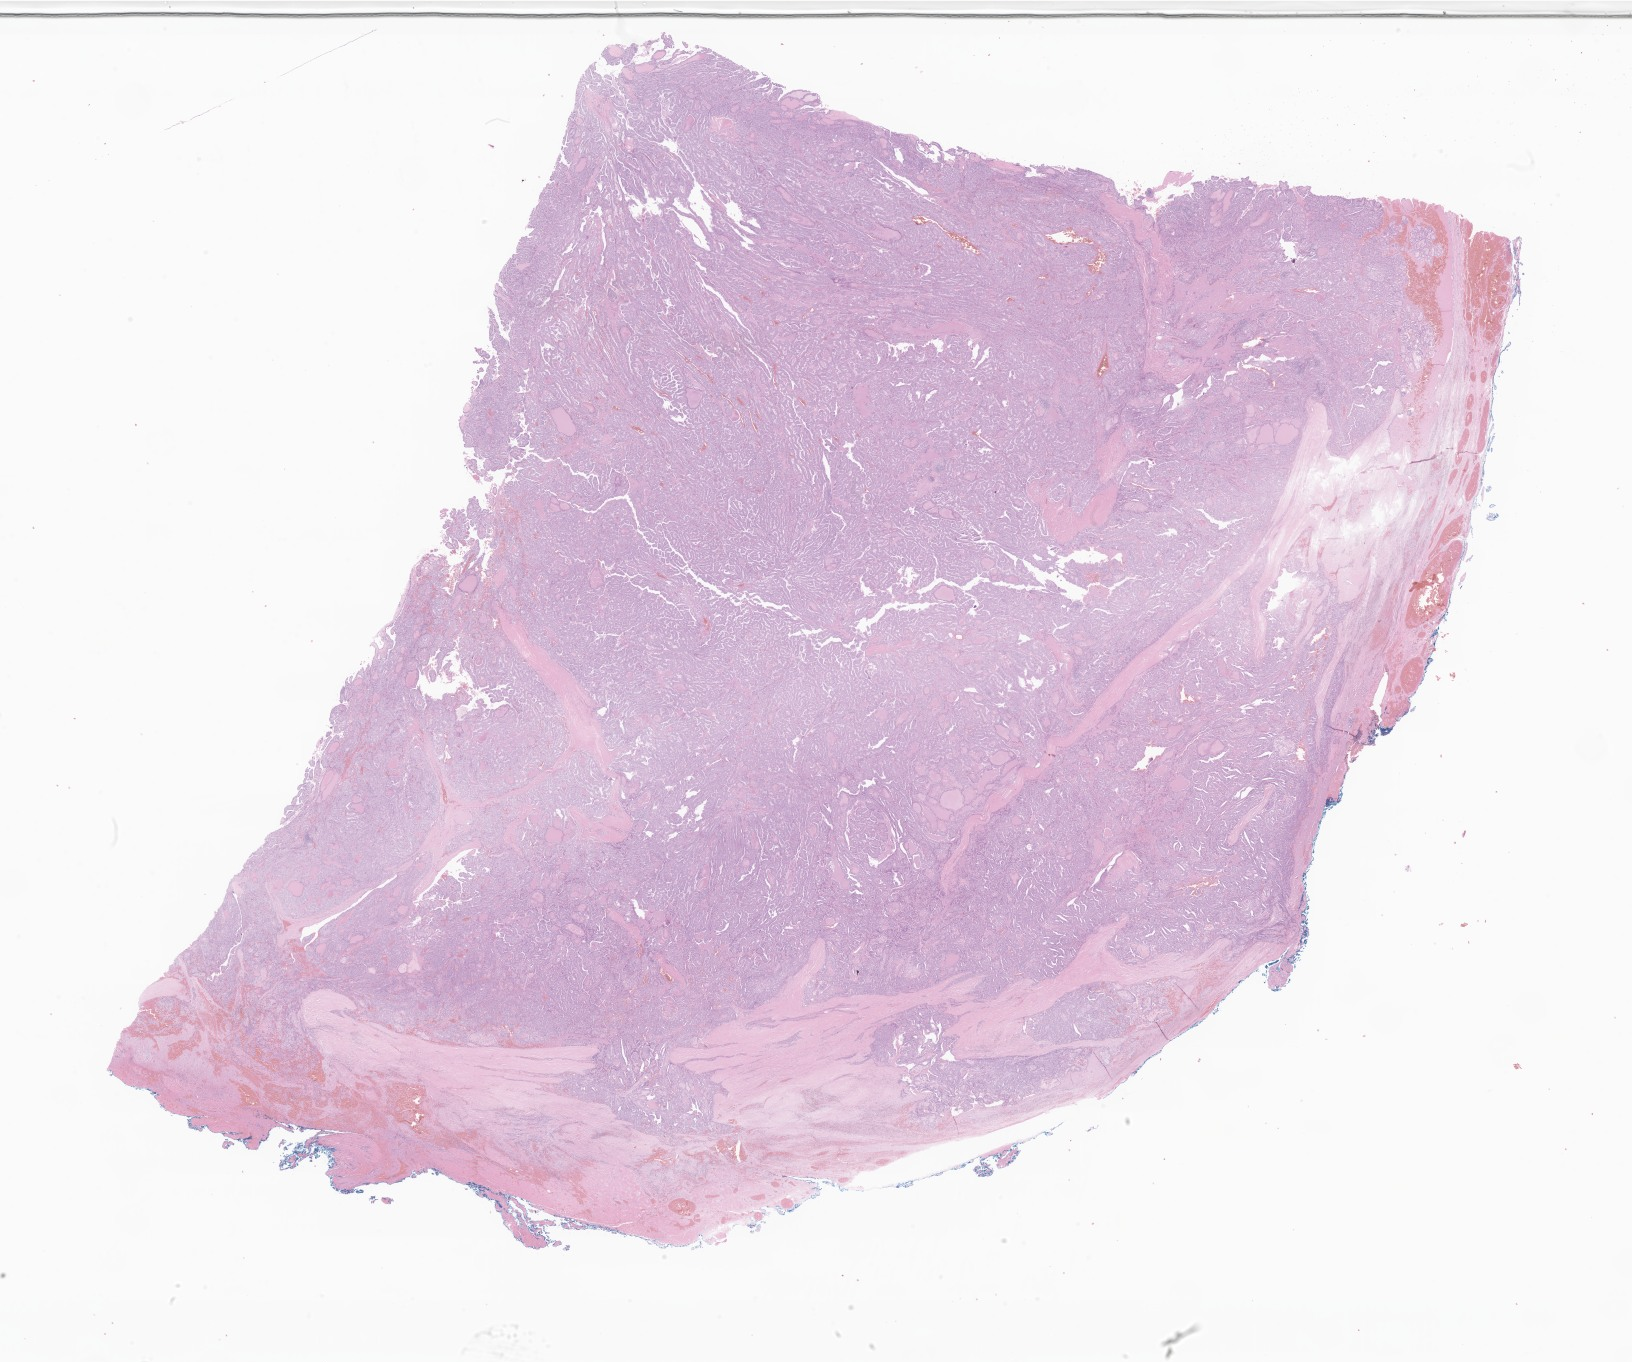
Whole-slide image, haematoxylin and eosin stain of tumor tissue from the thyroid — whole scanned area (about 27.5 x 23.0 mm) shown as a low-resolution overview. Formalin-fixed paraffin-embedded section. Female patient, age 192 months (16 years).
* diagnosis: Papillary carcinoma, NOS